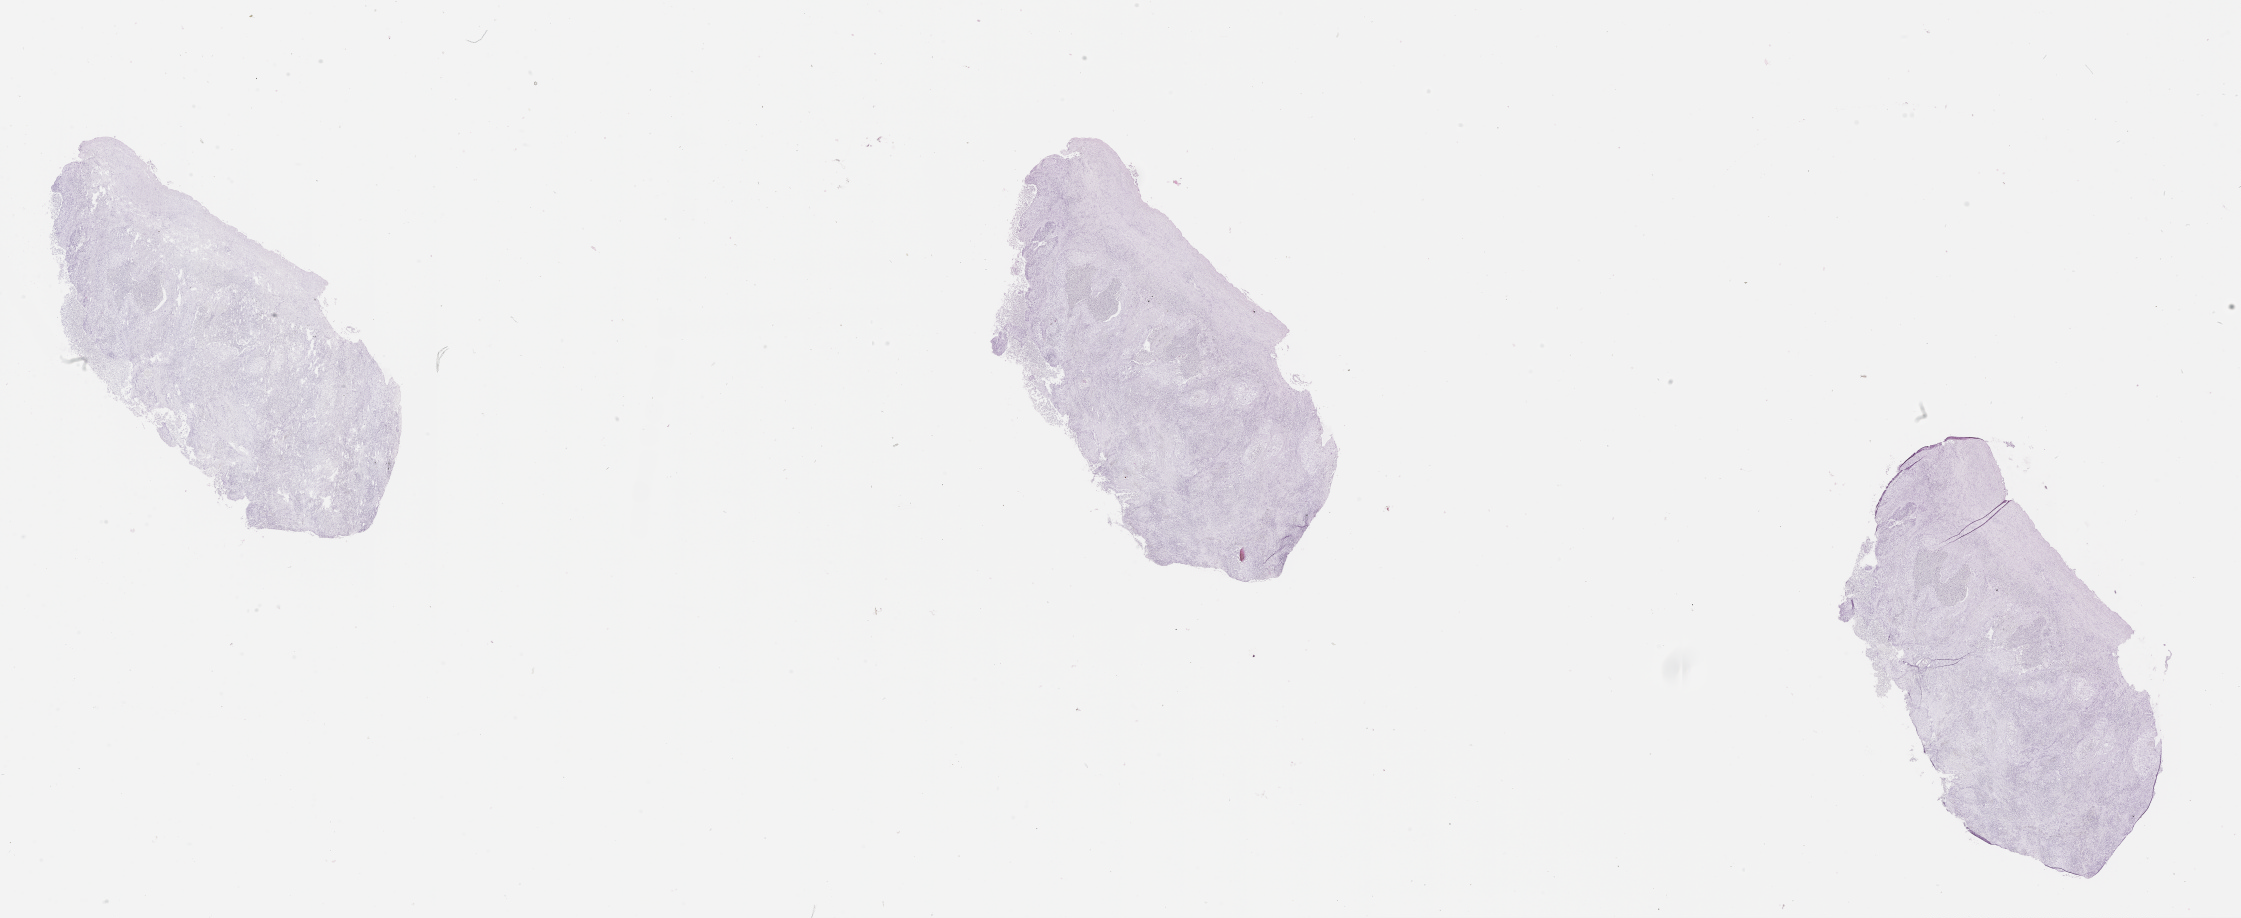
Digitized H&E tissue section (whole slide) — low-resolution overview of the scanned area, about 36.1 x 14.8 mm (slide scanned at 20x); lung, tumour tissue. 66-year-old male patient.
Patient diagnosis (cohort enrolment): squamous cell carcinoma (lung).